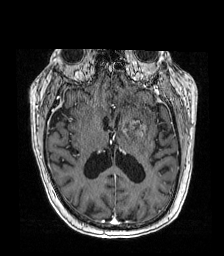
Brain MRI from a brain-tumour surgery series, one axial slice; position 83 of 192 along the scan axis; T1-weighted post-contrast; 1 mm slice thickness; 224 × 256 image matrix, field of view 219 × 250 mm. Case-level facts recorded for this patient, not image findings: histopathology: Metastatic carcinoma from lung primary; tumour location: Left Frontal Caudate.
Annotated regions visible in this slice (outlined manually by an expert reader):
- tumour: box from (x=117, y=115) to (x=148, y=138) px